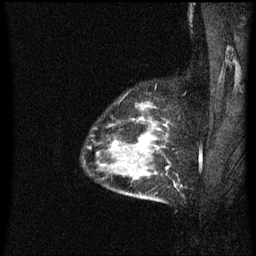
Breast MRI (dynamic contrast-enhanced), one sagittal slice; position 50 of 60 along the scan axis; dynamic contrast-enhanced series, image 2 of 3 at this slice position (ordered by acquisition); 1.5 T; TE 4.2 ms, TR 8.4 ms; 2 mm slice thickness; 256 × 256 image matrix. Female patient, age 34 years. Case-level facts recorded for this patient, not image findings: setting: breast cancer imaged before/during neoadjuvant chemotherapy; receptor status: HR-positive, HER2-negative.
Annotated regions visible in this slice (semi-automatic segmentation, software-assisted and operator-edited):
- analysis volume of interest (the breast-tissue region the enhancement analysis was run in; not a lesion): bounding box [x1, y1, x2, y2] px = [86, 104, 170, 203]
- tumour enhancement mask (voxels above the 70 % enhancement threshold inside the analysis volume of interest): [110, 118, 155, 167]